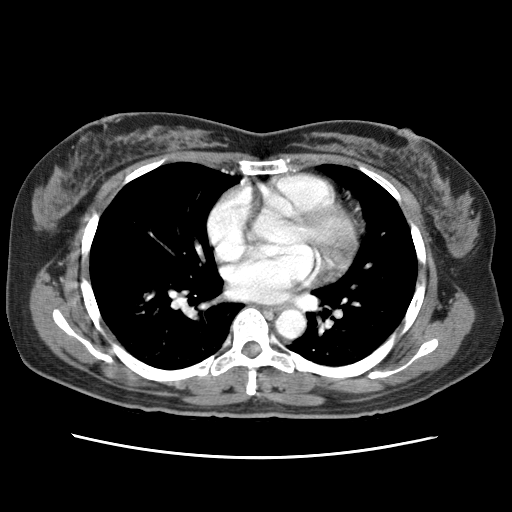
Contrast-enhanced abdominal CT (liver protocol), one axial slice. Slice 79 of 79 in the series (ordered by position). Reconstruction kernel STANDARD. 120 kVp. Soft-tissue window (W 400 / L 40 HU). 512 × 512 image matrix, field of view 340 × 340 mm. Case-level facts recorded for this patient, not image findings: diagnosis: hepatocellular carcinoma (patient treated with transarterial chemoembolisation; whether this scan precedes or follows treatment is not stated here); TNM stage (as recorded): Stage-I; Child-Pugh class: A.
Structures marked on this image (semi-automatically segmented with operator editing):
- abdominal aorta: bounding box (x1, y1, x2, y2) in pixels: (275, 309, 306, 339)